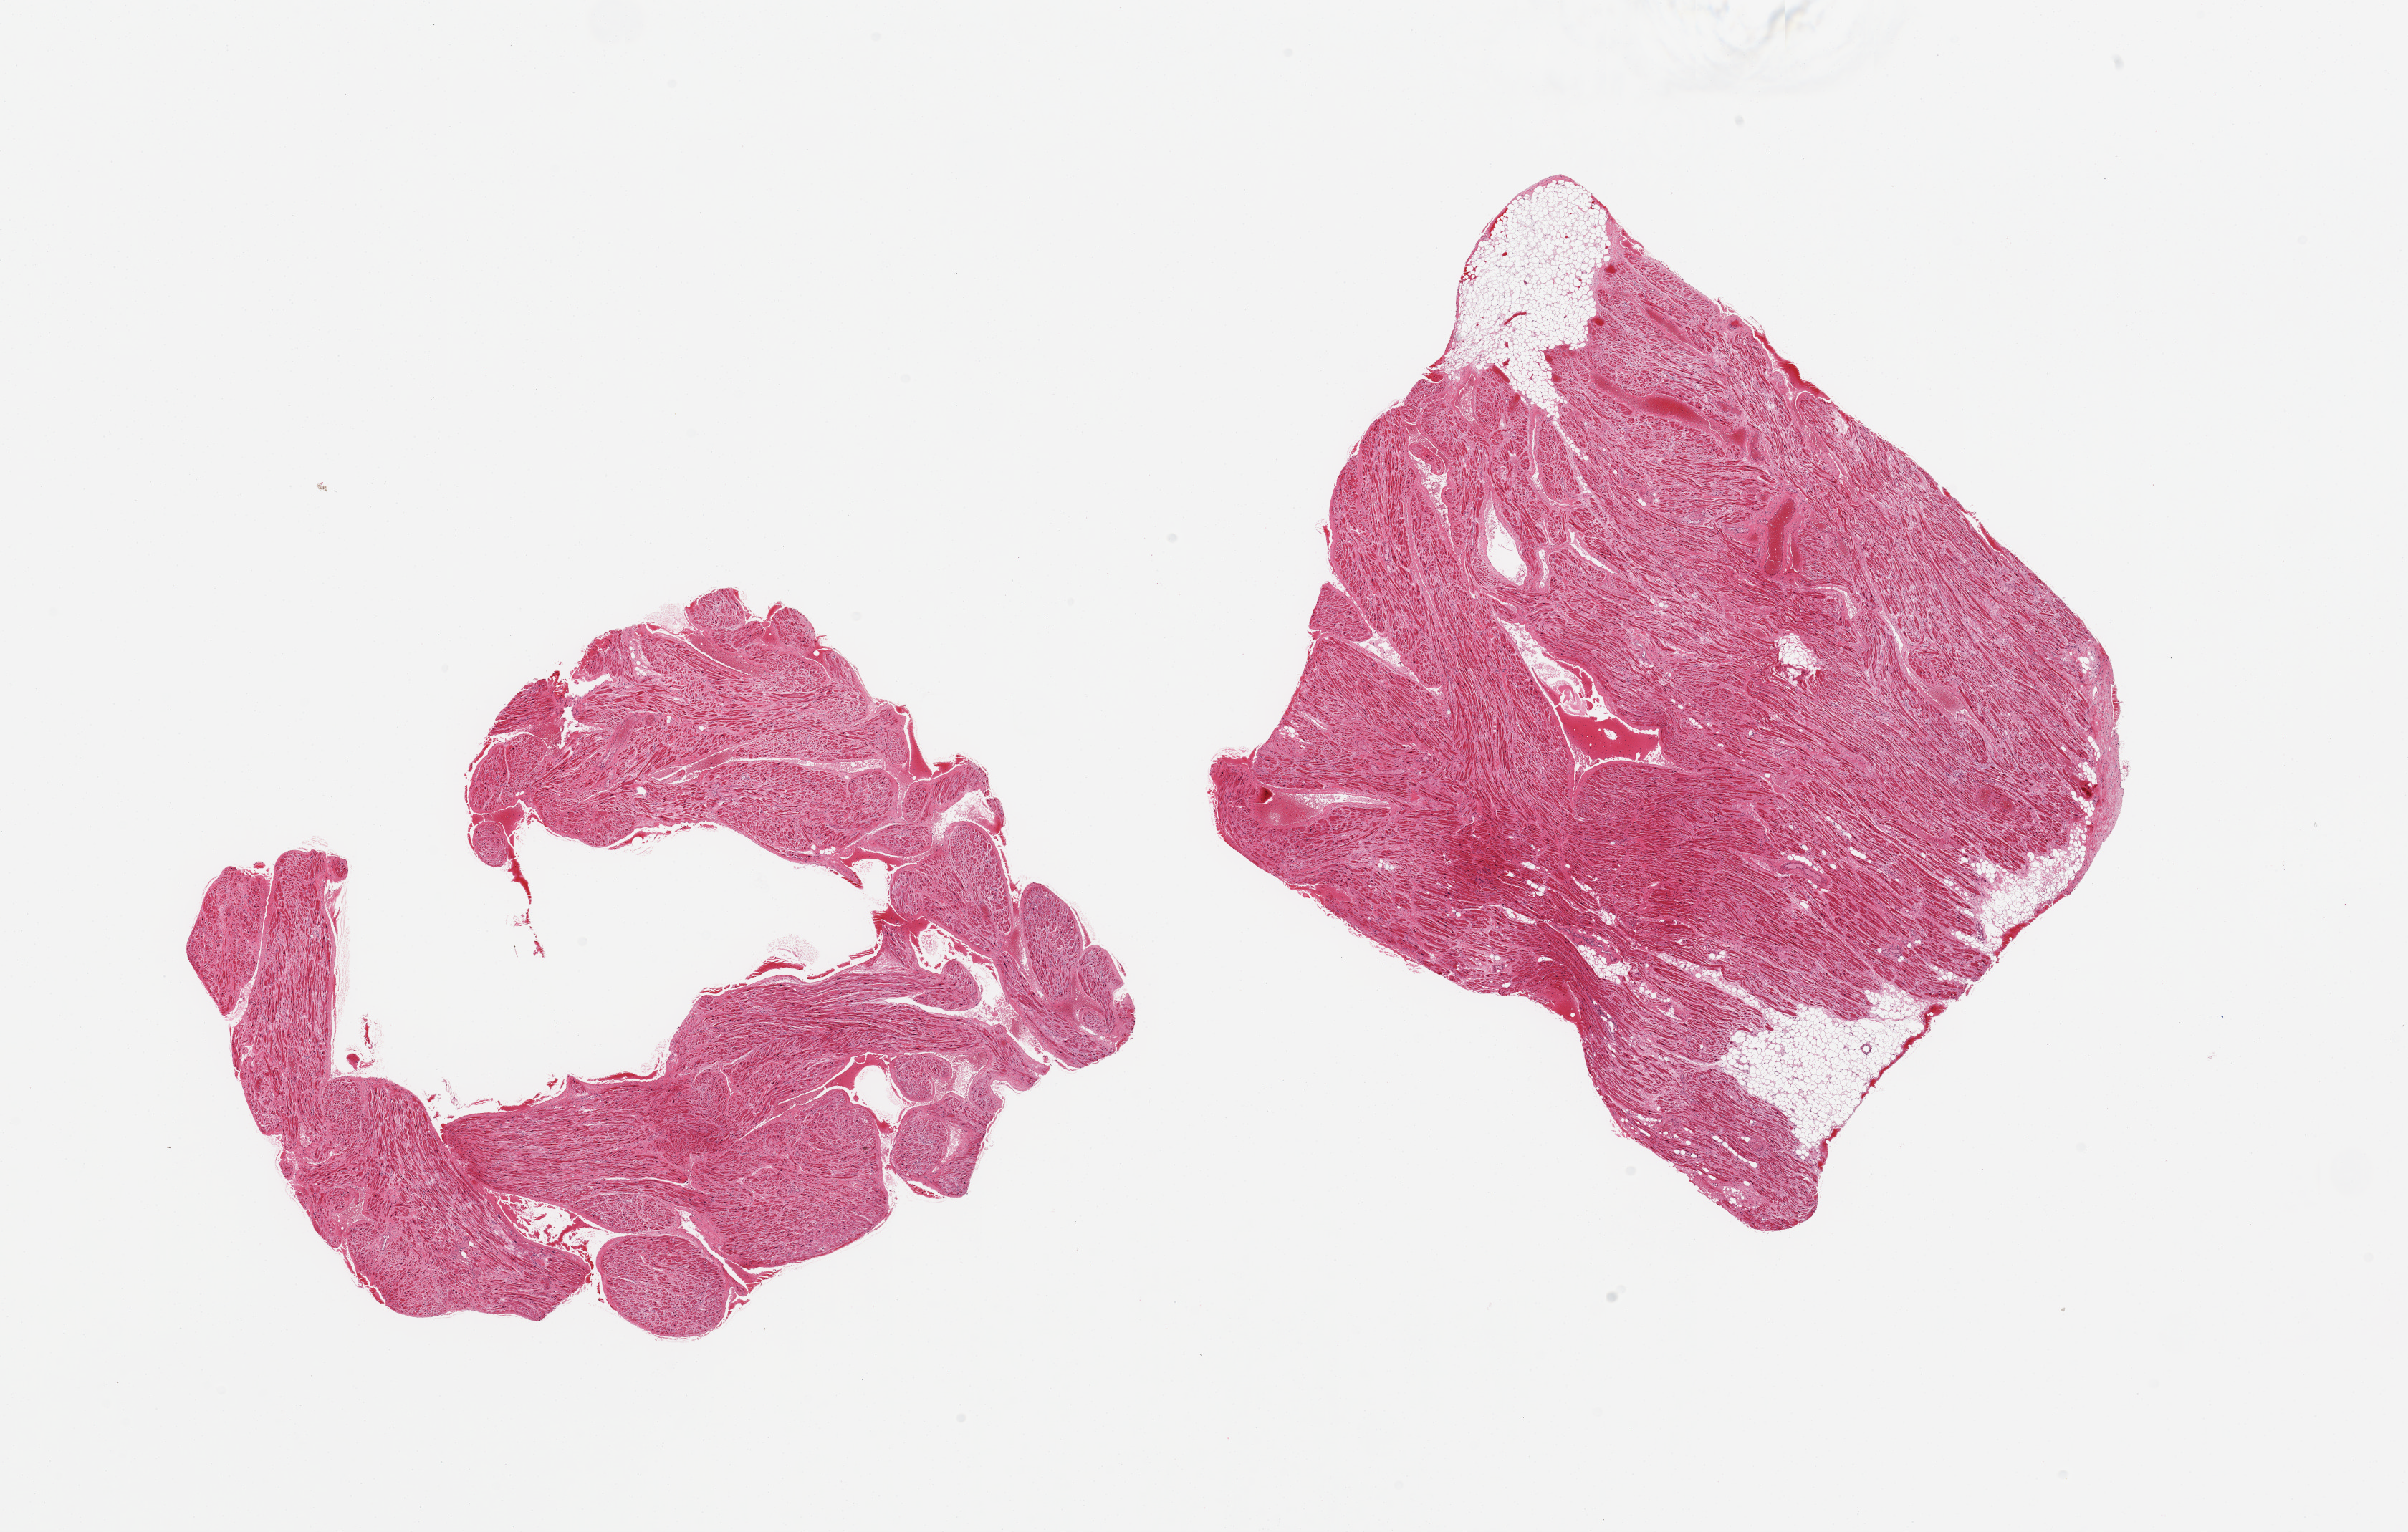
Haematoxylin and eosin whole-slide image — whole scanned area (about 26.6 x 16.9 mm, acquisition: 20x scan) shown as a low-resolution overview; PAXgene-fixed, paraffin-embedded tissue; section of auricular appendage (target tissue); donor tissue sample. Donor: female.
- pathologist's review note for this sample: 2 pieces; well trimmed, 95% muscle